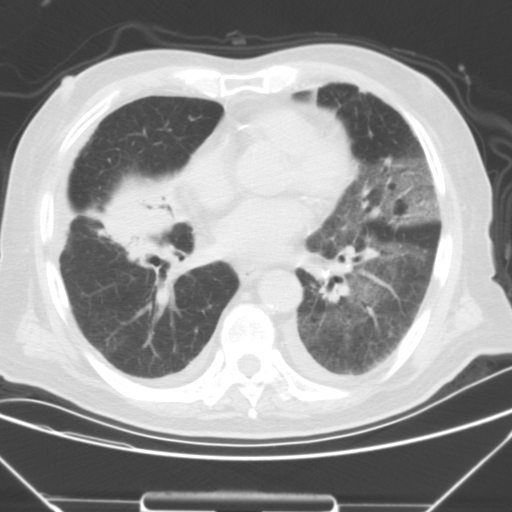
Chest CT, one axial slice; position 14 of 43 along the scan axis; 120 kVp; lung window (W 1500 / L -600 HU); 512 × 512 image matrix, field of view 343 × 343 mm. Male patient, age 85 years. From the clinical record (not read from this slice): clinical TNM (as recorded): T4 N3 M2.
Annotated regions visible in this slice (rectangle marked by the reading radiologist):
- lung tumour (recorded histology: squamous cell carcinoma): bounding box (x1, y1, x2, y2) in pixels: (89, 175, 191, 255)